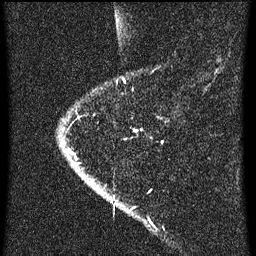
Breast MRI (dynamic contrast-enhanced), one sagittal slice. Slice 8 of 60 in the series (ordered by position). Dynamic contrast-enhanced series, image 2 of 3 at this slice position (ordered by acquisition). 1.5 T. TE 4.2 ms, TR 8 ms. 256 × 256 image matrix. Female patient, age 47 years.
Outlined on this slice (semi-automatic segmentation, software-assisted and operator-edited):
- analysis volume of interest (the breast-tissue region the enhancement analysis was run in; not a lesion): box from (x=56, y=78) to (x=160, y=193) px
- tumour enhancement mask (voxels above the 70 % enhancement threshold inside the analysis volume of interest): (x=69, y=152)–(x=75, y=157)